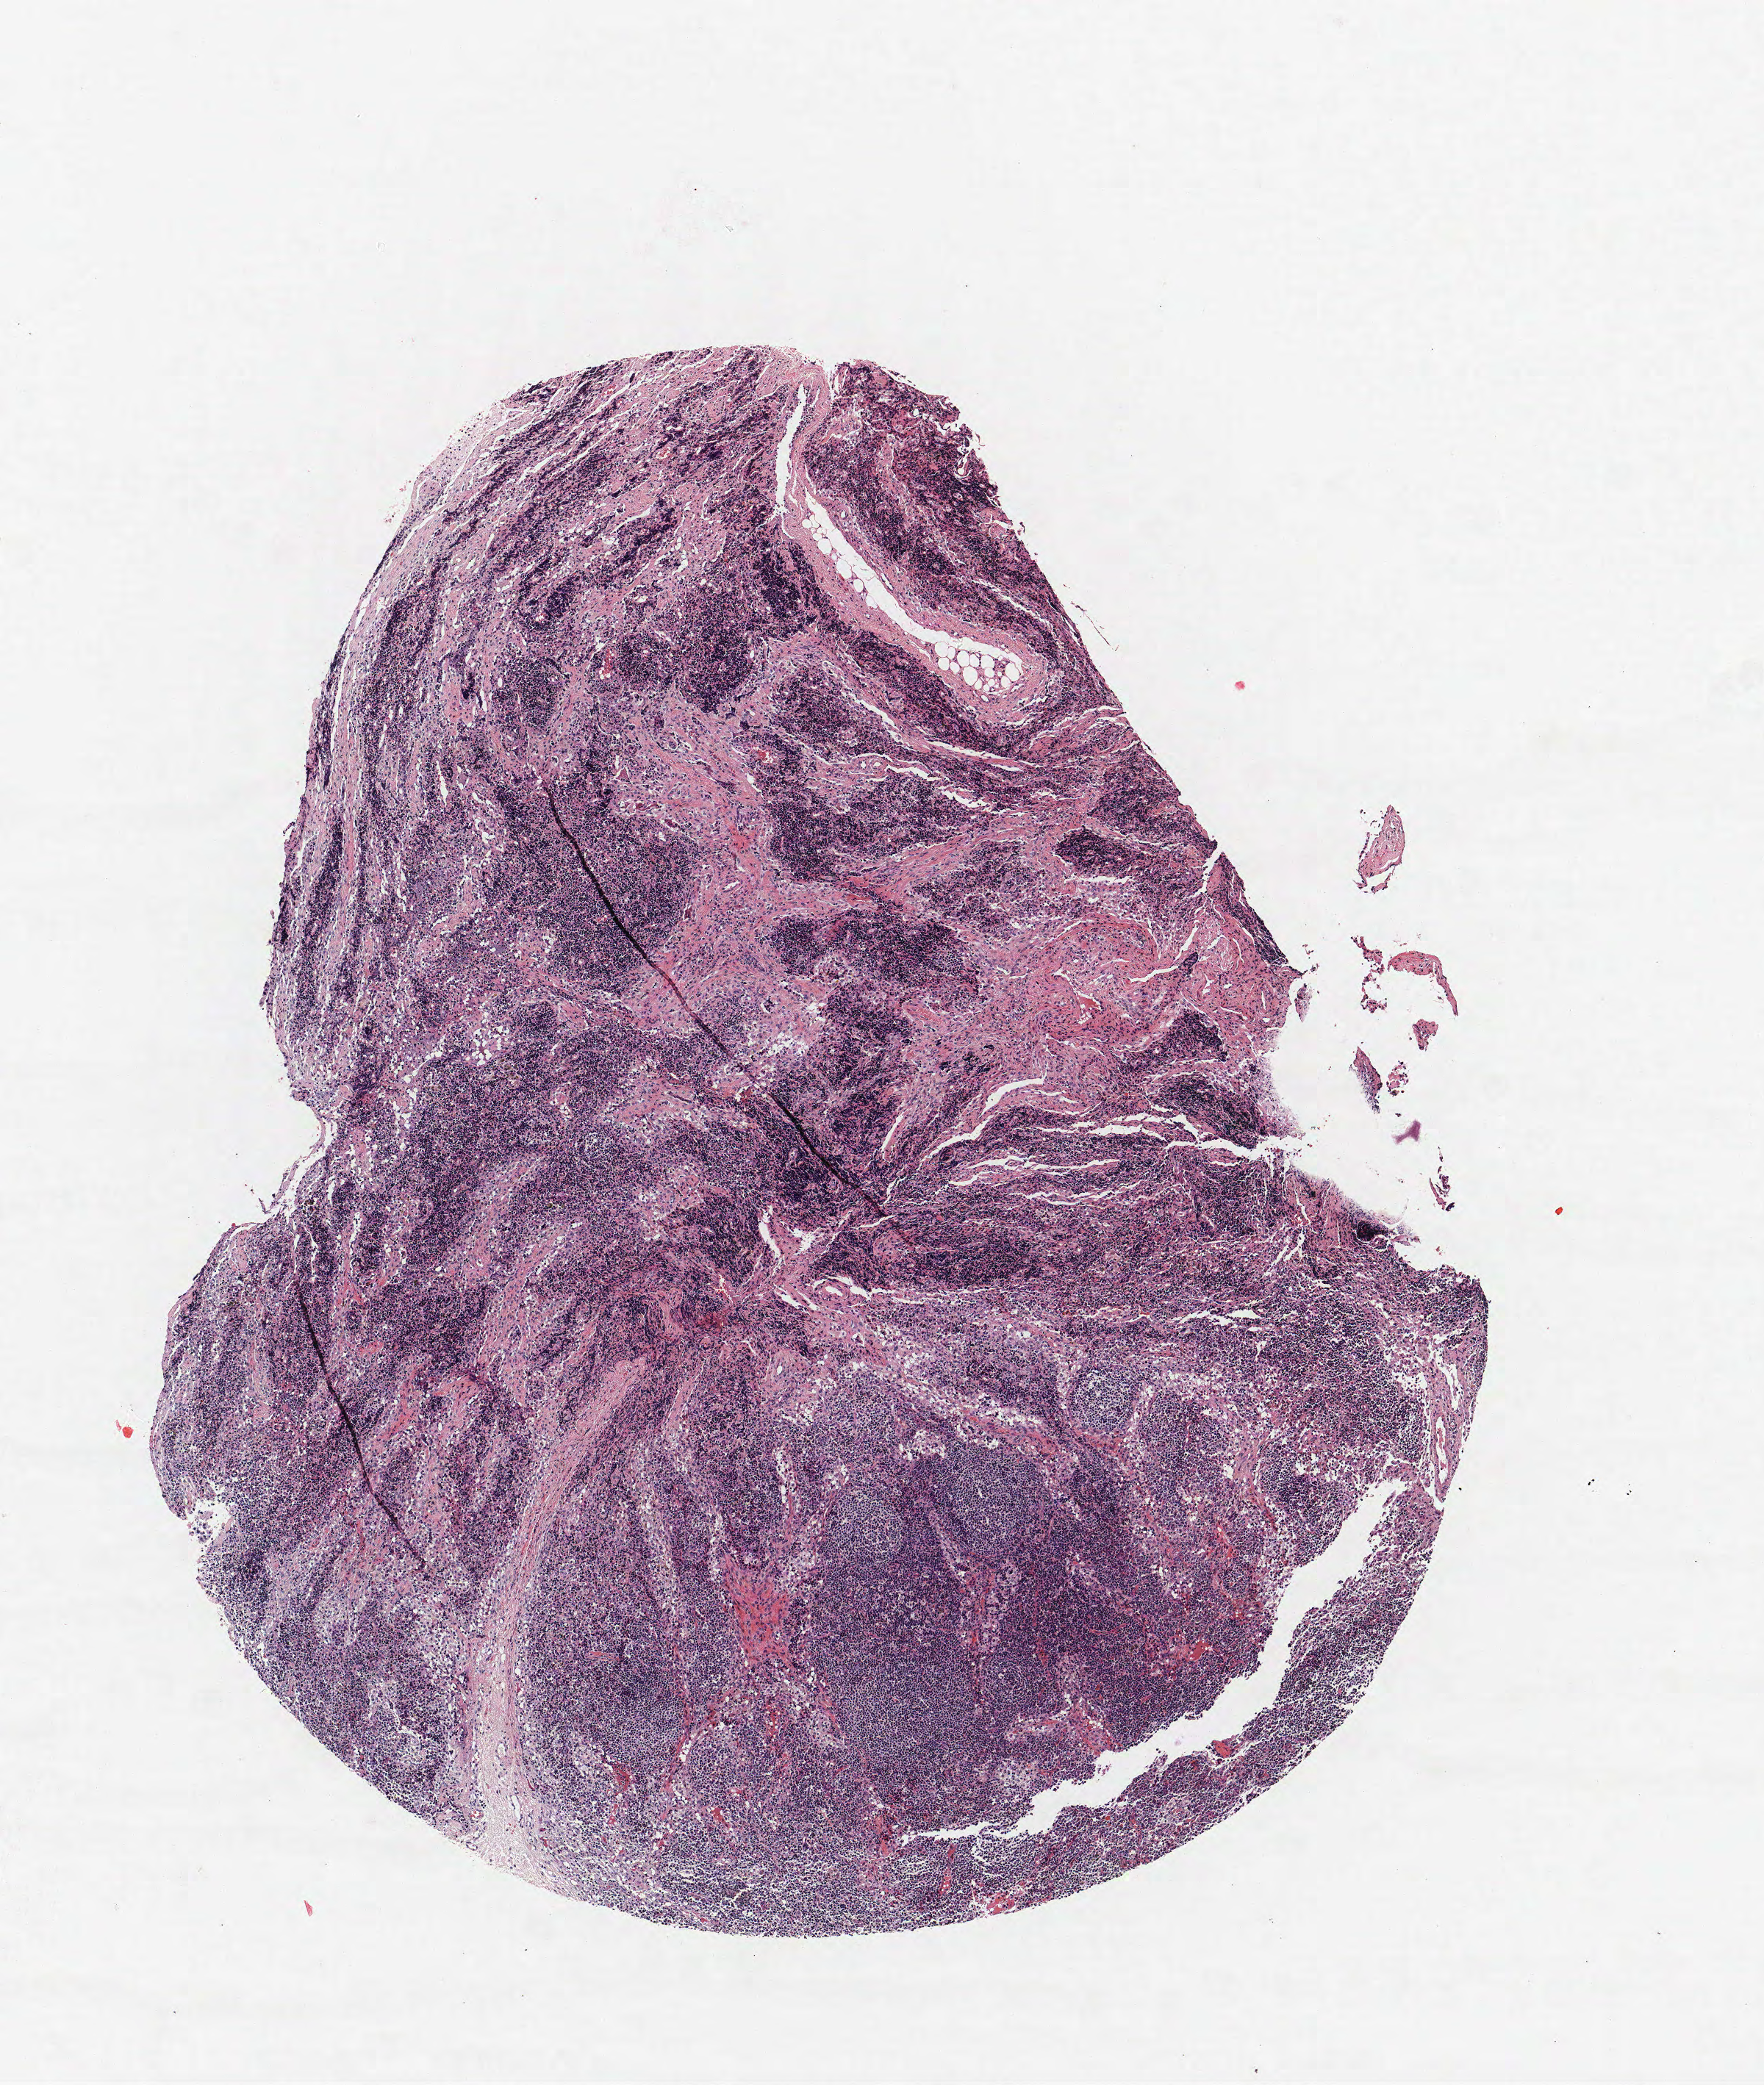
H&E whole-slide image — low-resolution overview of the scanned area, about 4.8 x 5.7 mm, FFPE section, lung. Male, age 57 at enrolment. Current smoker at enrolment. Grade: cannot be assessed (GX).
- ICD-O-3 topography: main bronchus (C34.0)
- primary tumour location (clinical record): left hilum
- stage (AJCC 6th edition): IV
- participant's lung-cancer diagnosis: Squamous cell carcinoma, NOS (ICD-O-3 8070/3)